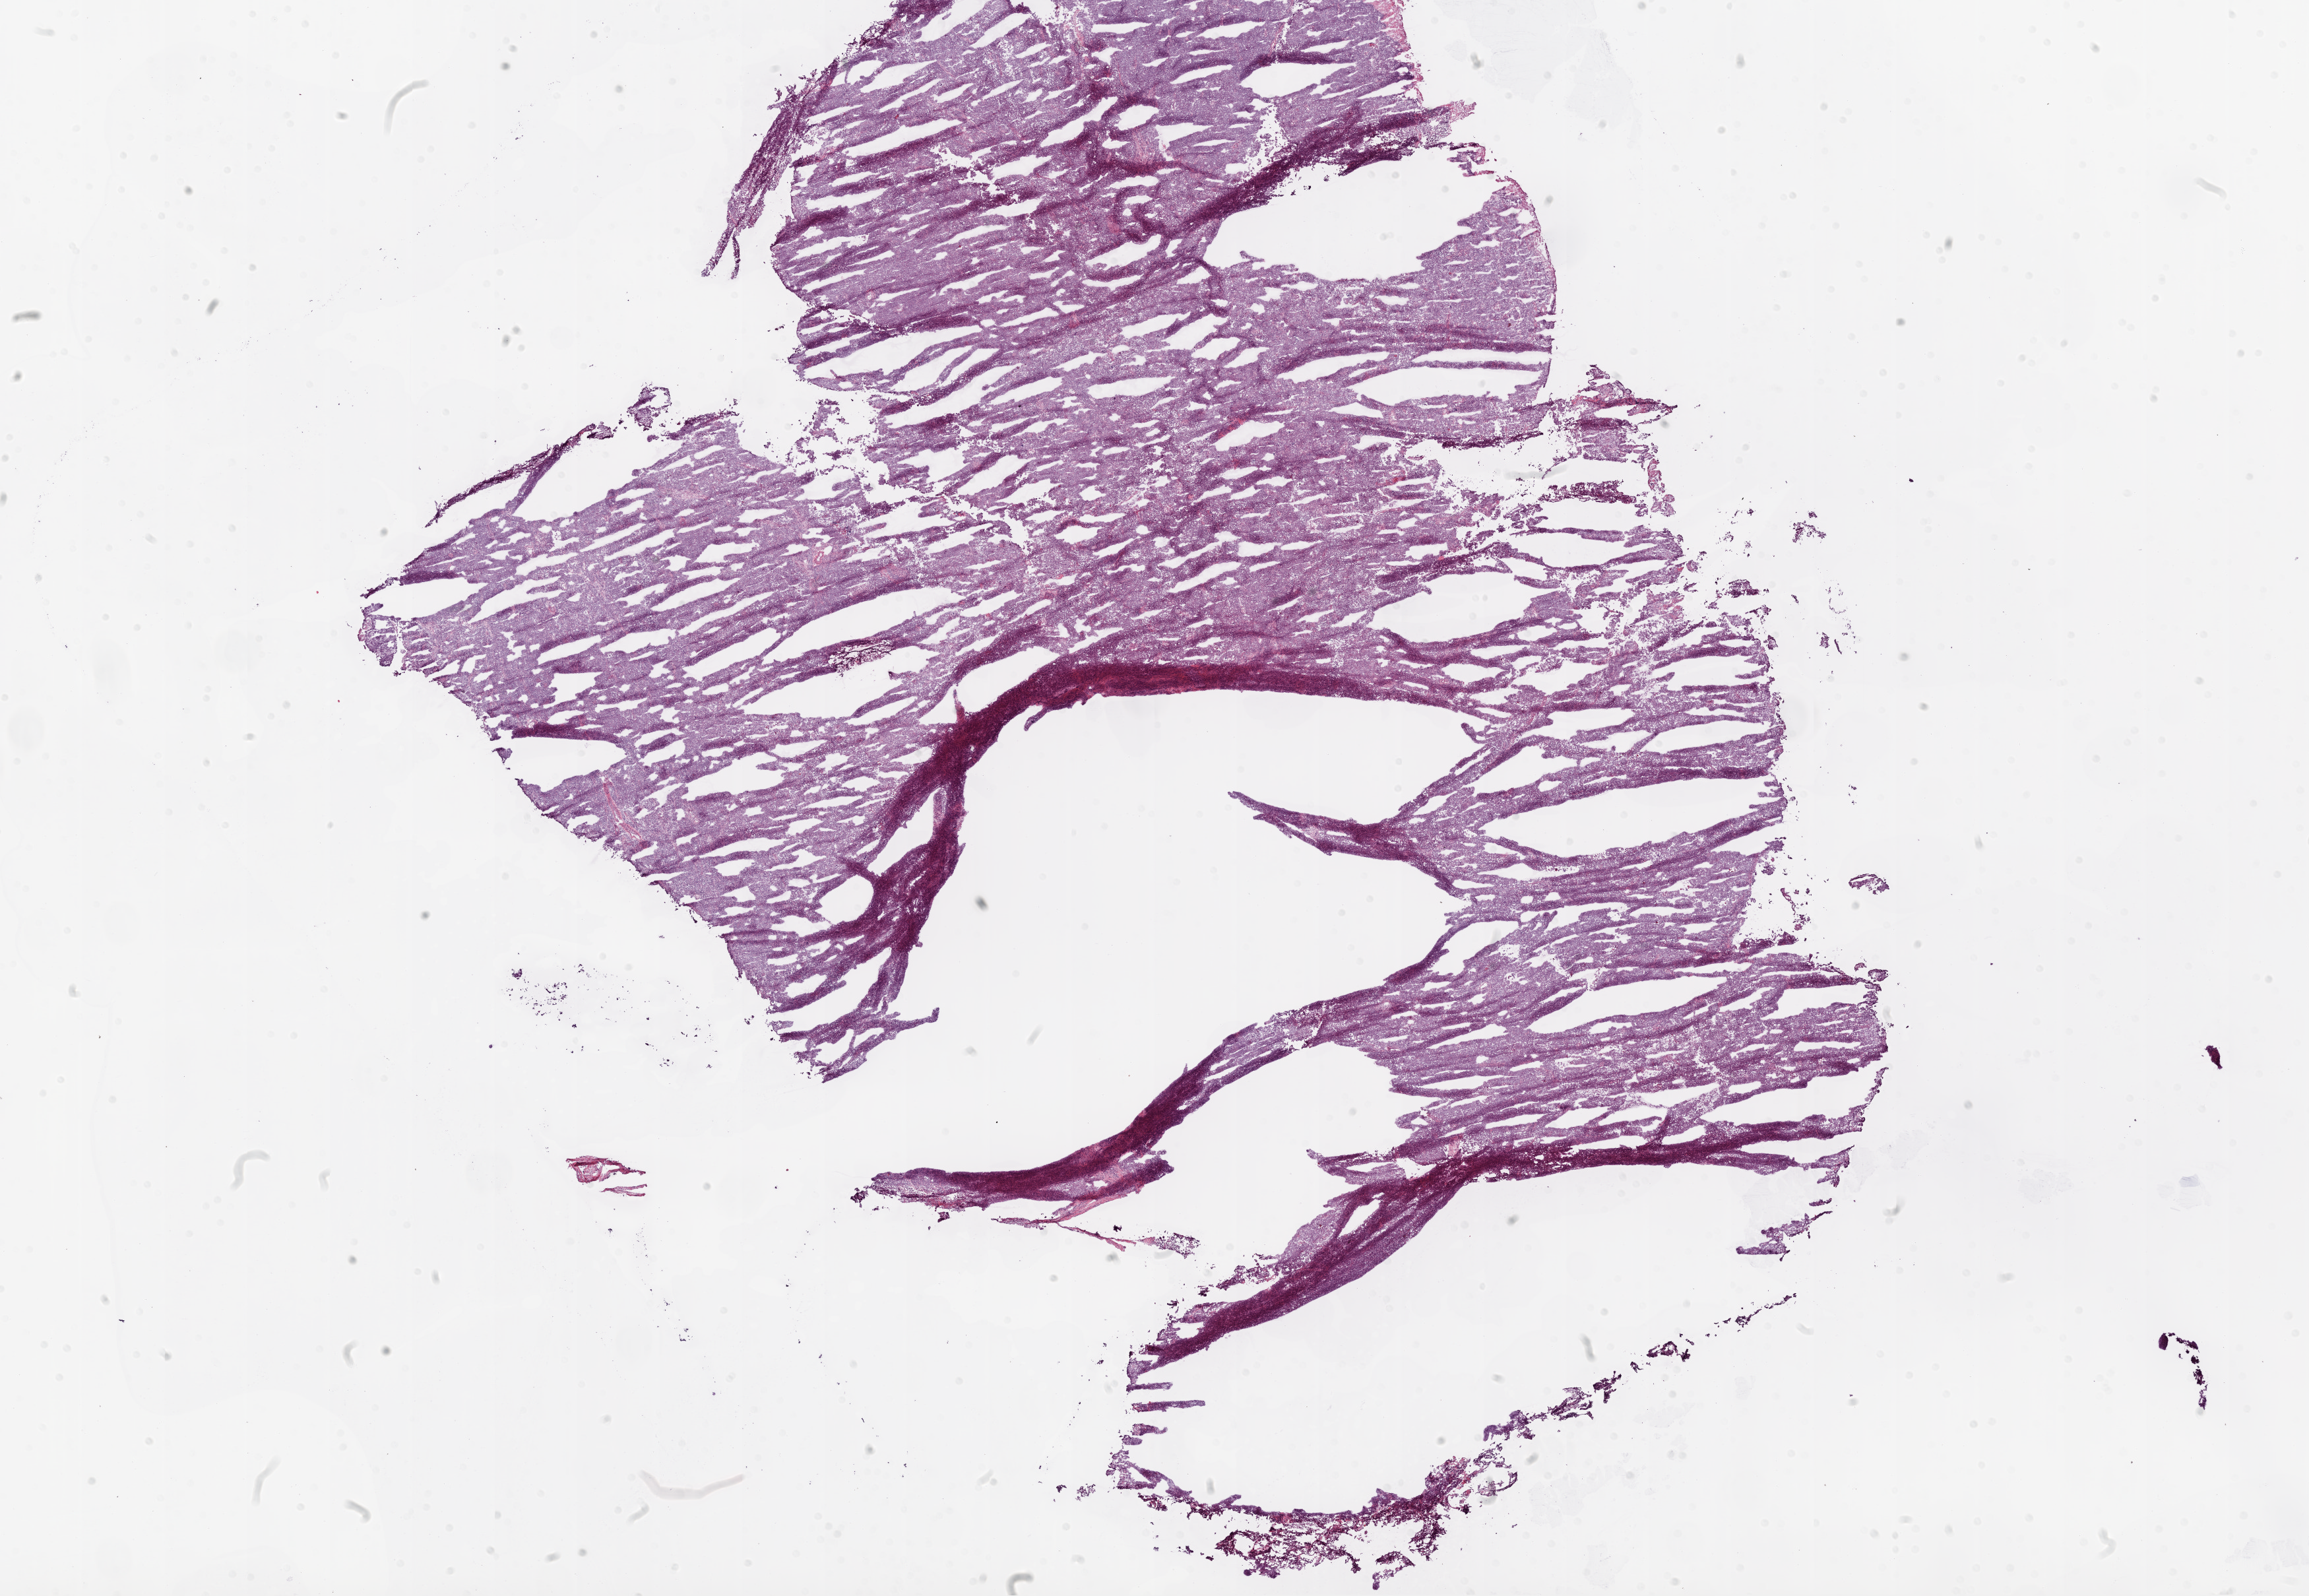
Digitized H&E tissue section (whole slide) — whole scanned area (about 28.1 x 19.4 mm) shown as a low-resolution overview; frozen section; primary tumour sample from the ovary. Patient: female, age at initial diagnosis 77 years. Histologic grade: G3 (poorly differentiated). Slide review estimates, as recorded: tumour cells 94%, tumour nuclei 95%, normal cells 0%, stromal cells 5%, necrosis 1%.
Diagnosis: Serous cystadenocarcinoma, NOS. FIGO stage: IIB.